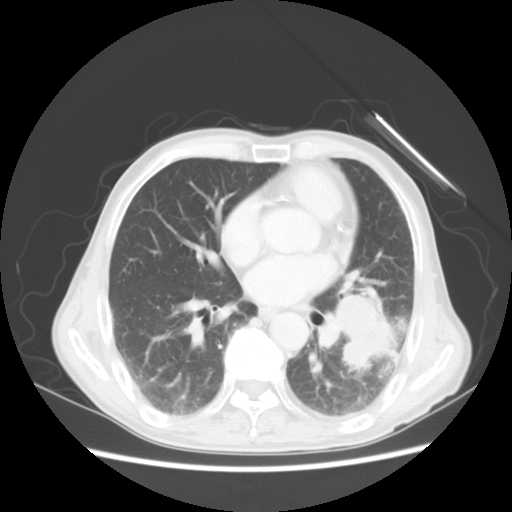
Chest CT, one axial slice. Slice 24 of 51 in the series (ordered by position). Reconstruction kernel STANDARD. 120 kVp. Lung window (W 1500 / L -600 HU). 5 mm slice thickness. 512 × 512 image matrix, field of view 360 × 360 mm. Patient: male, 64 years. From the clinical record (not read from this slice): clinical TNM (as recorded): T4 N0 M0; histopathological grade: G2-3.
Outlined on this slice (rectangle marked by the reading radiologist):
- lung tumour (recorded histology: squamous cell carcinoma): box from (x=322, y=292) to (x=409, y=375) px